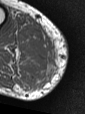
MRI of an extremity soft-tissue mass, one axial slice; slice 34 of 47 in the series (ordered by position); MR volume resampled by the dataset authors to the PET/CT grid (not the native acquisition matrix); 85 × 114 image matrix, field of view 83 × 111 mm. Male patient. From the clinical record (not read from this slice): histological type: pleiomorphic liposarcoma; grade: high; site of the primary tumour: right calf.
Outlined on this slice (expert contour drawn on MRI and transferred to this co-registered scan by the dataset authors):
- gross tumour volume including surrounding oedema: box from (x=36, y=32) to (x=53, y=70) px